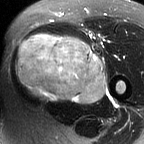
MRI of an extremity soft-tissue mass, one axial slice; slice 35 of 60 in the series (ordered by position); T2-weighted fat-saturated; MR volume resampled by the dataset authors to the PET/CT grid (not the native acquisition matrix); 3.27 mm slice thickness; 144 × 144 image matrix, field of view 141 × 141 mm. Female patient. From the clinical record (not read from this slice): histological type: pleiomorphic leiomyosarcoma; grade: intermediate; site of the primary tumour: left thigh.
Annotated regions visible in this slice (expert contour drawn on MRI and transferred to this co-registered scan by the dataset authors):
- gross tumour volume including surrounding oedema: box from (x=15, y=33) to (x=105, y=105) px
- gross tumour volume (mass): (x=15, y=35)–(x=105, y=103)